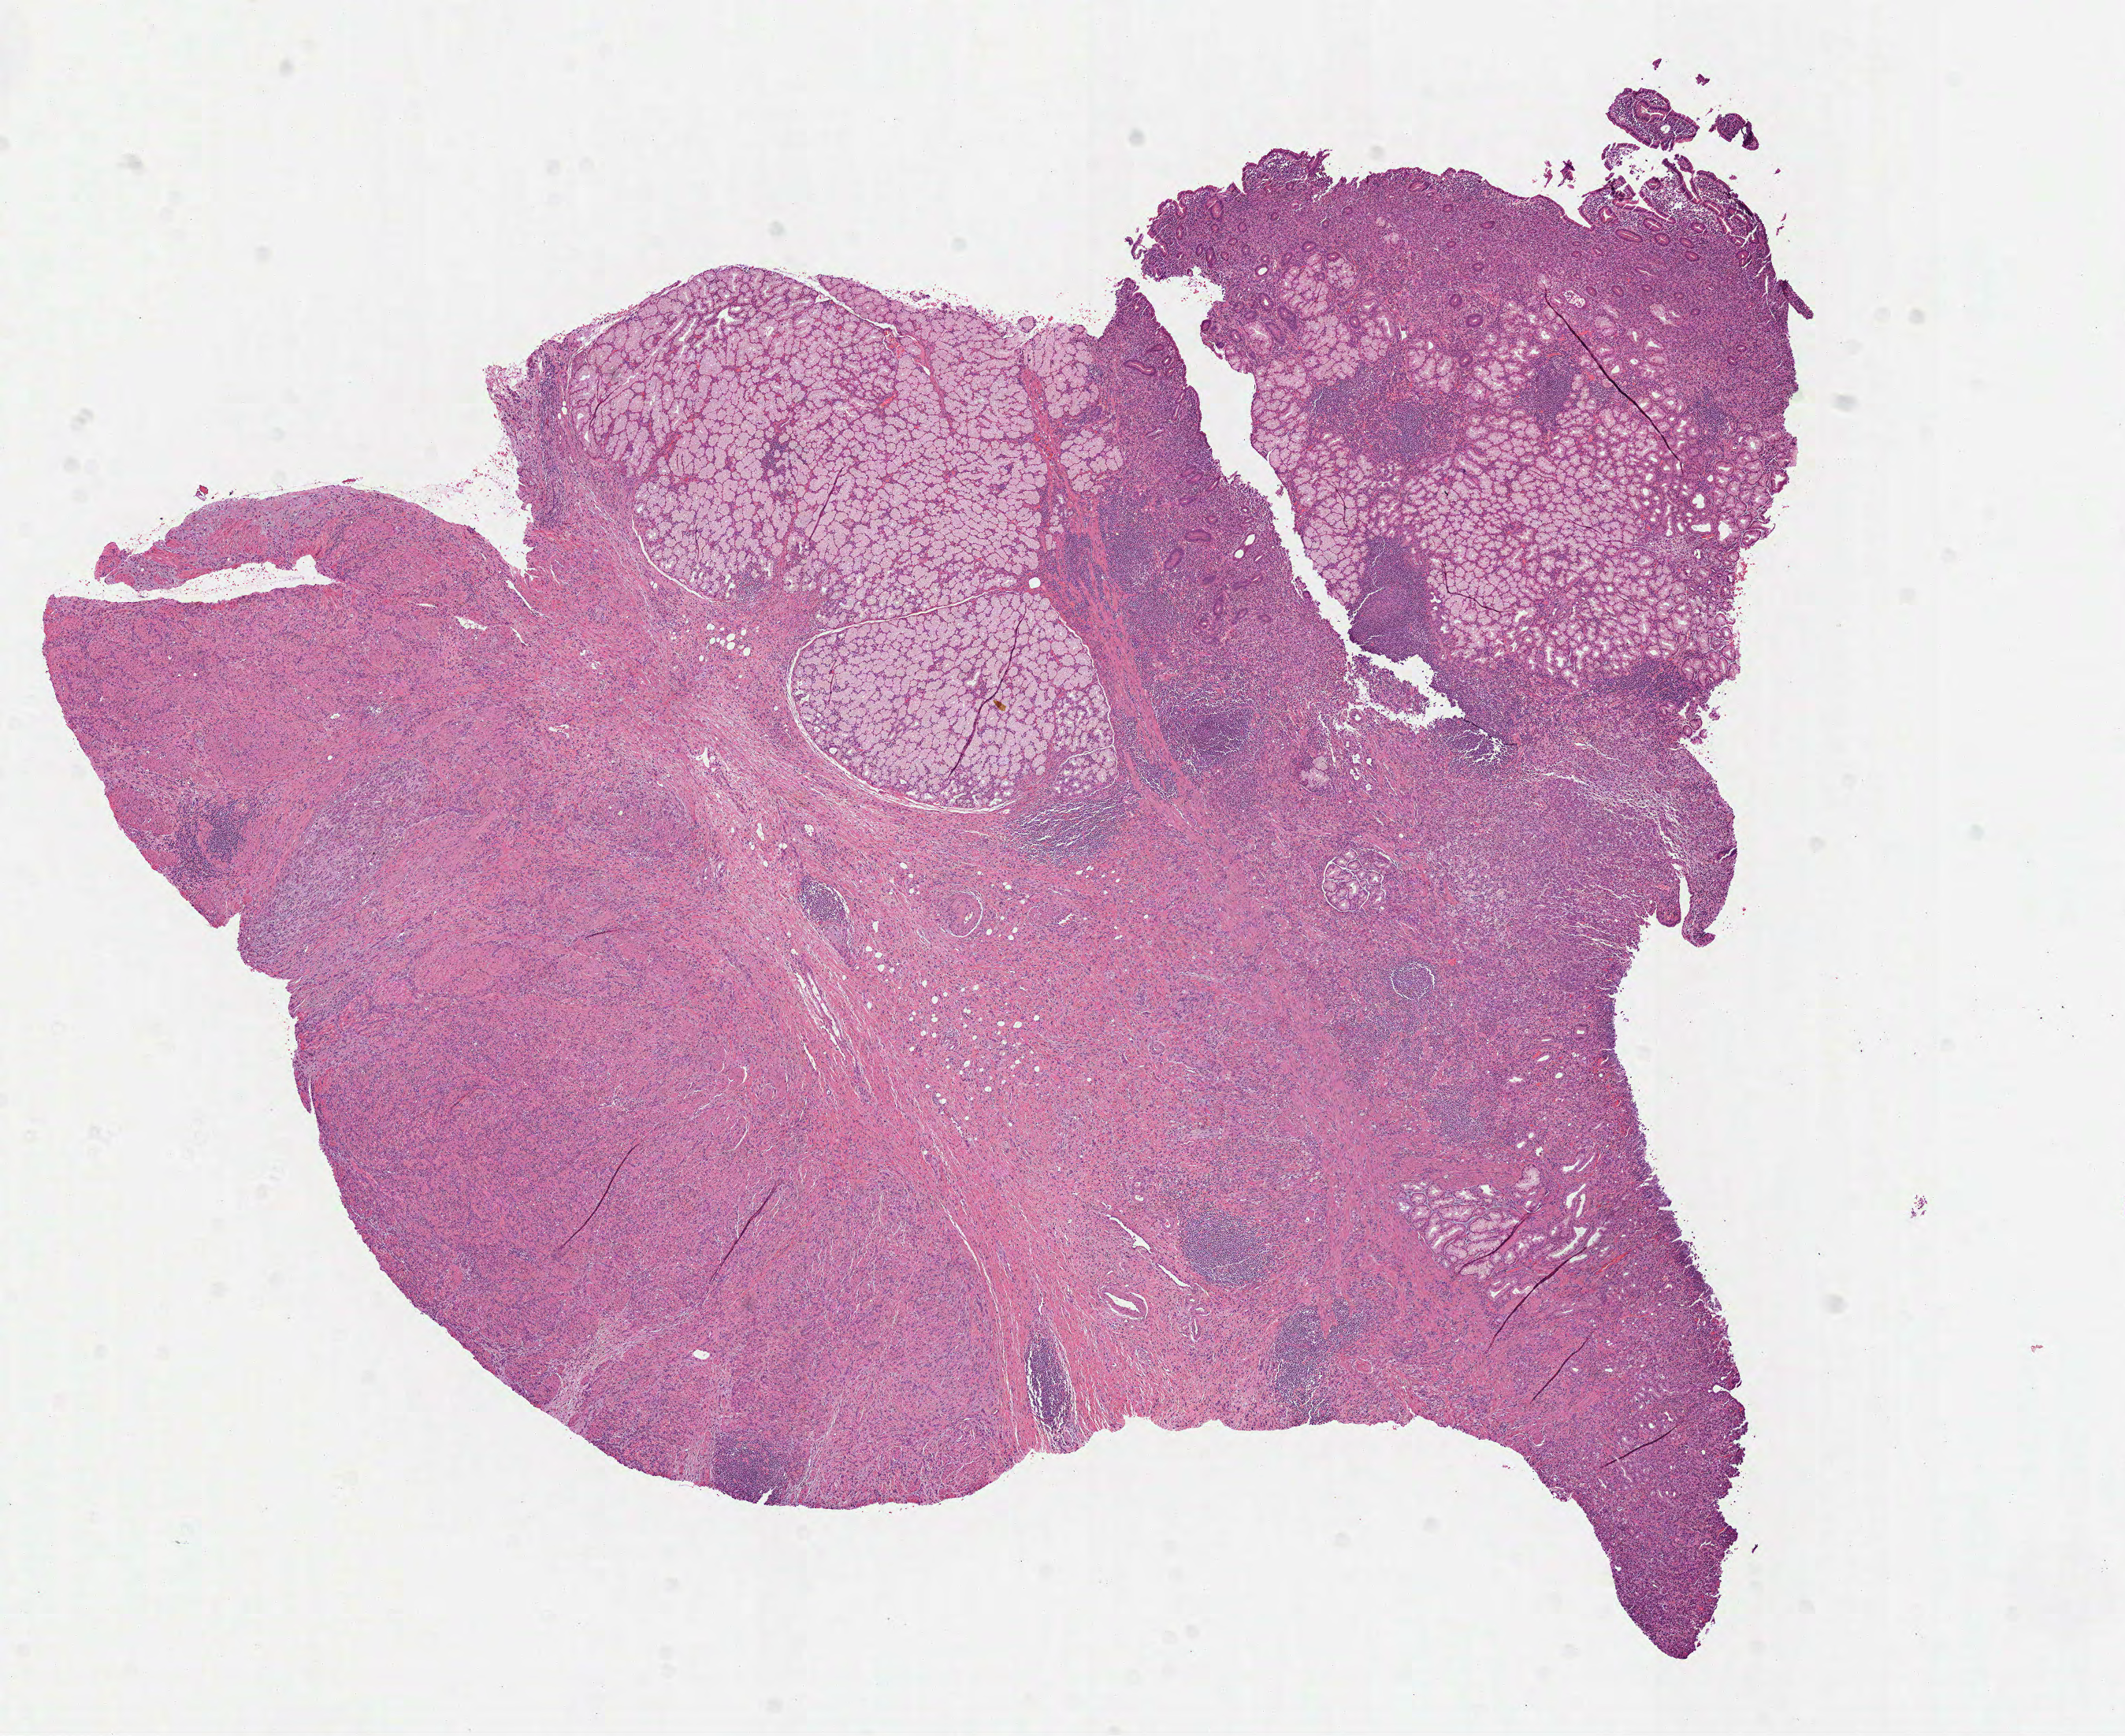
Hematoxylin and eosin (H&E) stained whole-slide image — low-resolution overview of the scanned area, about 10.9 x 8.9 mm; FFPE section; stomach, primary tumour sample. Male patient; age at initial diagnosis 48 years. Histologic grade: G3 (poorly differentiated).
AJCC pathologic stage: IIIA (6th edition). Histologic diagnosis: Carcinoma, diffuse type (gastric antrum).